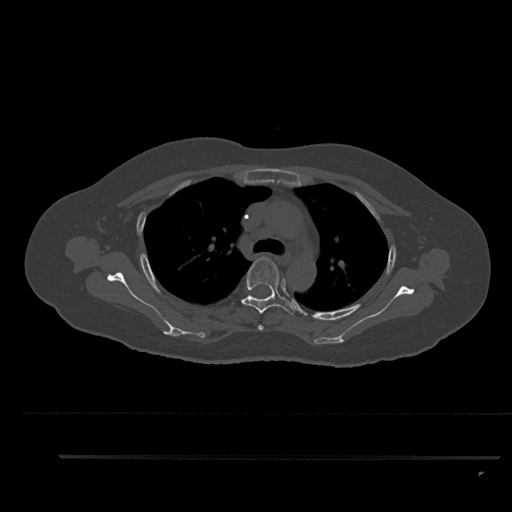
CT including the spine, one axial slice. Reconstruction kernel Br40s/3. Bone window (W 1800 / L 400 HU). 0.5 mm slice thickness. 512 × 512 image matrix, field of view 408 × 408 mm. Patient: female, 44 years. Case-level facts recorded for this patient, not image findings: primary cancer: renal.
Annotated regions visible in this slice (semi-automatically segmented with operator editing):
- T3 vertebra: bounding box (x1, y1, x2, y2) in pixels: (258, 325, 264, 331)
- T4 vertebra: (241, 257, 296, 315)